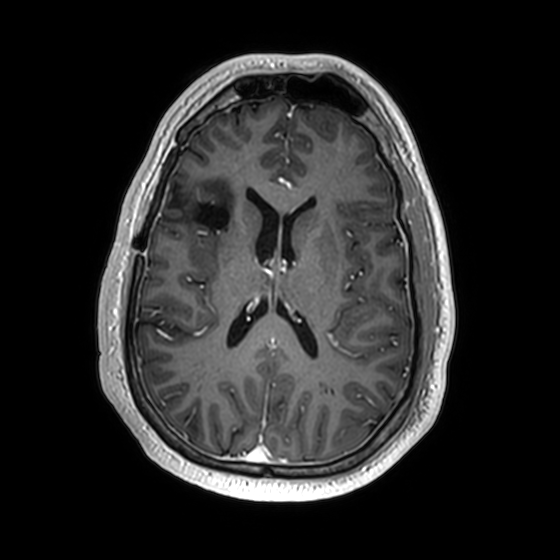
Brain MRI from a brain-tumour surgery series, one axial slice; slice 77 of 174 in the series (ordered by position); T1-weighted post-contrast; 1 mm slice thickness; 560 × 560 image matrix, field of view 256 × 256 mm. Case-level facts recorded for this patient, not image findings: histopathology: Astrocytoma; WHO grade: 2; IDH mutation: yes; tumour location: Right Insular.
Outlined on this slice (expert manual segmentation):
- previous resection cavity: bounding box <173,196,229,231> (left, top, right, bottom; pixels)